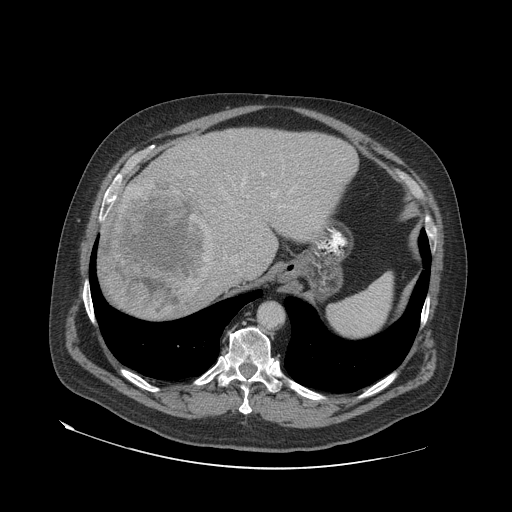
Contrast-enhanced abdominal CT (liver protocol), one axial slice. Position 55 of 79 along the scan axis. 140 kVp. Soft-tissue window (W 400 / L 40 HU). 2.5 mm slice thickness. 512 × 512 image matrix, field of view 480 × 480 mm. From the clinical record (not read from this slice): diagnosis: hepatocellular carcinoma (patient treated with transarterial chemoembolisation; whether this scan precedes or follows treatment is not stated here); TNM stage (as recorded): Stage-IVA; Child-Pugh class: A.
Annotated regions visible in this slice (semi-automatic segmentation, software-assisted and operator-edited):
- abdominal aorta: bounding box <259,303,283,328> (left, top, right, bottom; pixels)
- liver parenchyma outside the tumour (the mass and vessels are separate outlines, so this box may not span the whole liver): <100,128,358,318>
- mass: <101,182,216,316>
- liver vessels: <242,172,275,197>